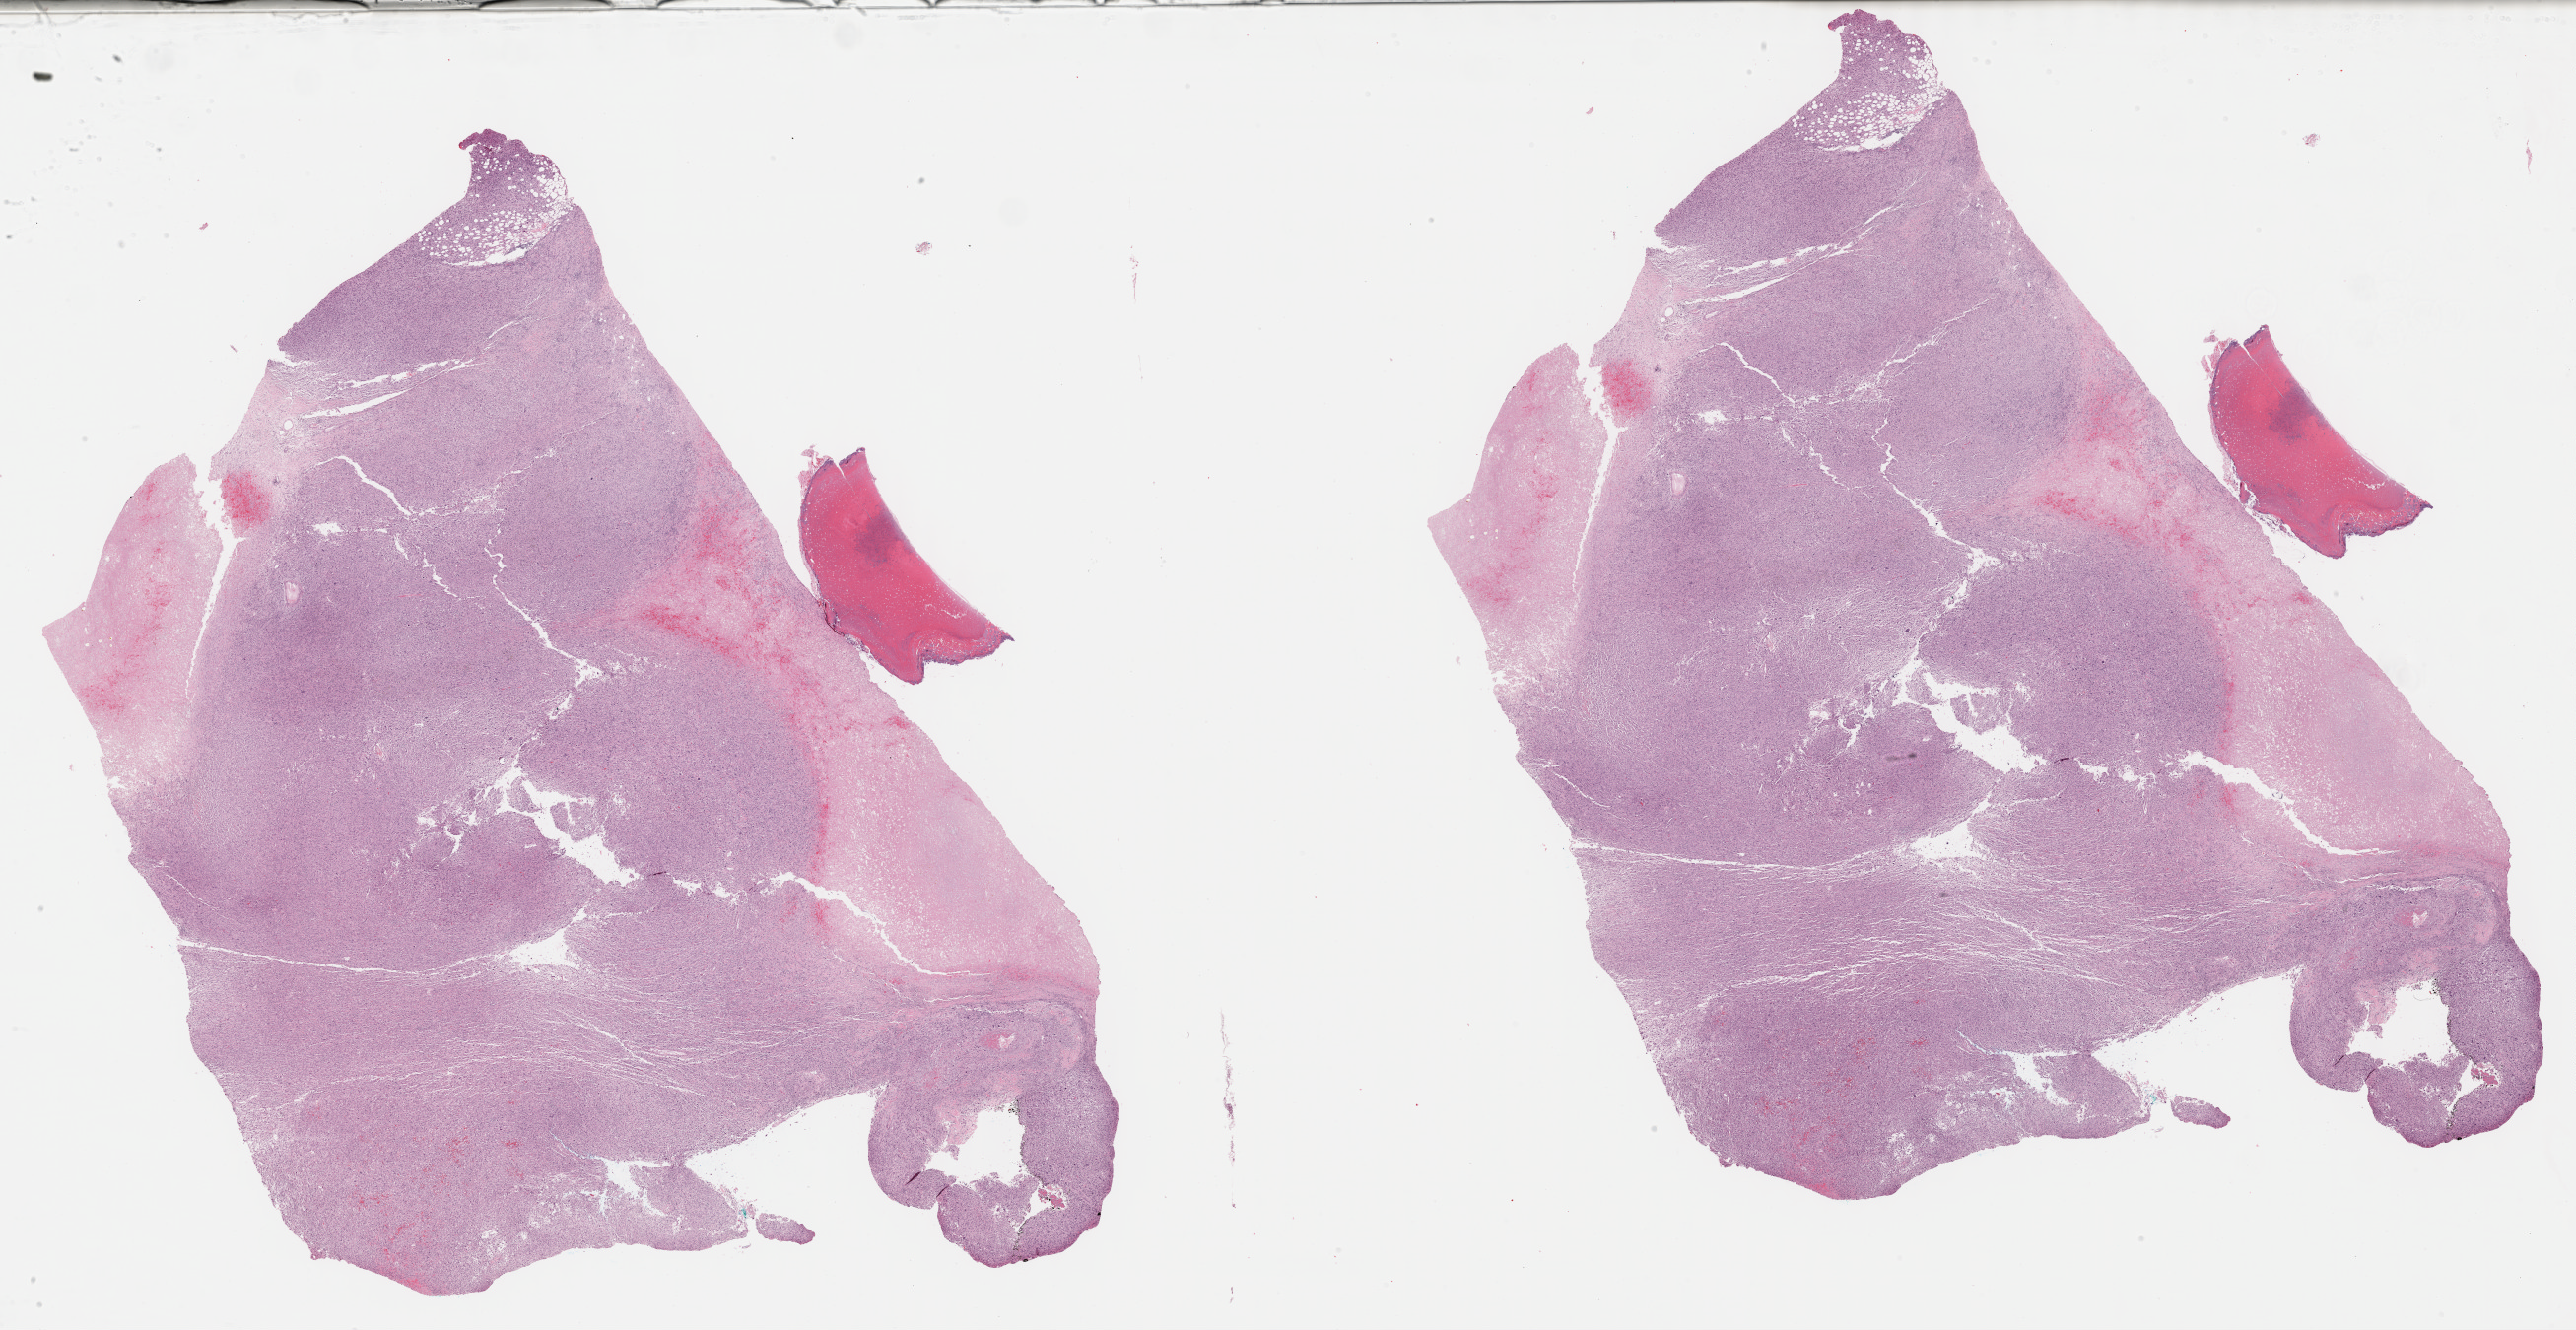
H&E whole-slide image, shown as a low-resolution overview of the whole scanned area (about 42.3 x 21.8 mm), FFPE section, connective, subcutaneous and other soft tissues, primary tumour sample. Female patient; age at initial diagnosis 65 years.
* histologic diagnosis: Malignant fibrous histiocytoma